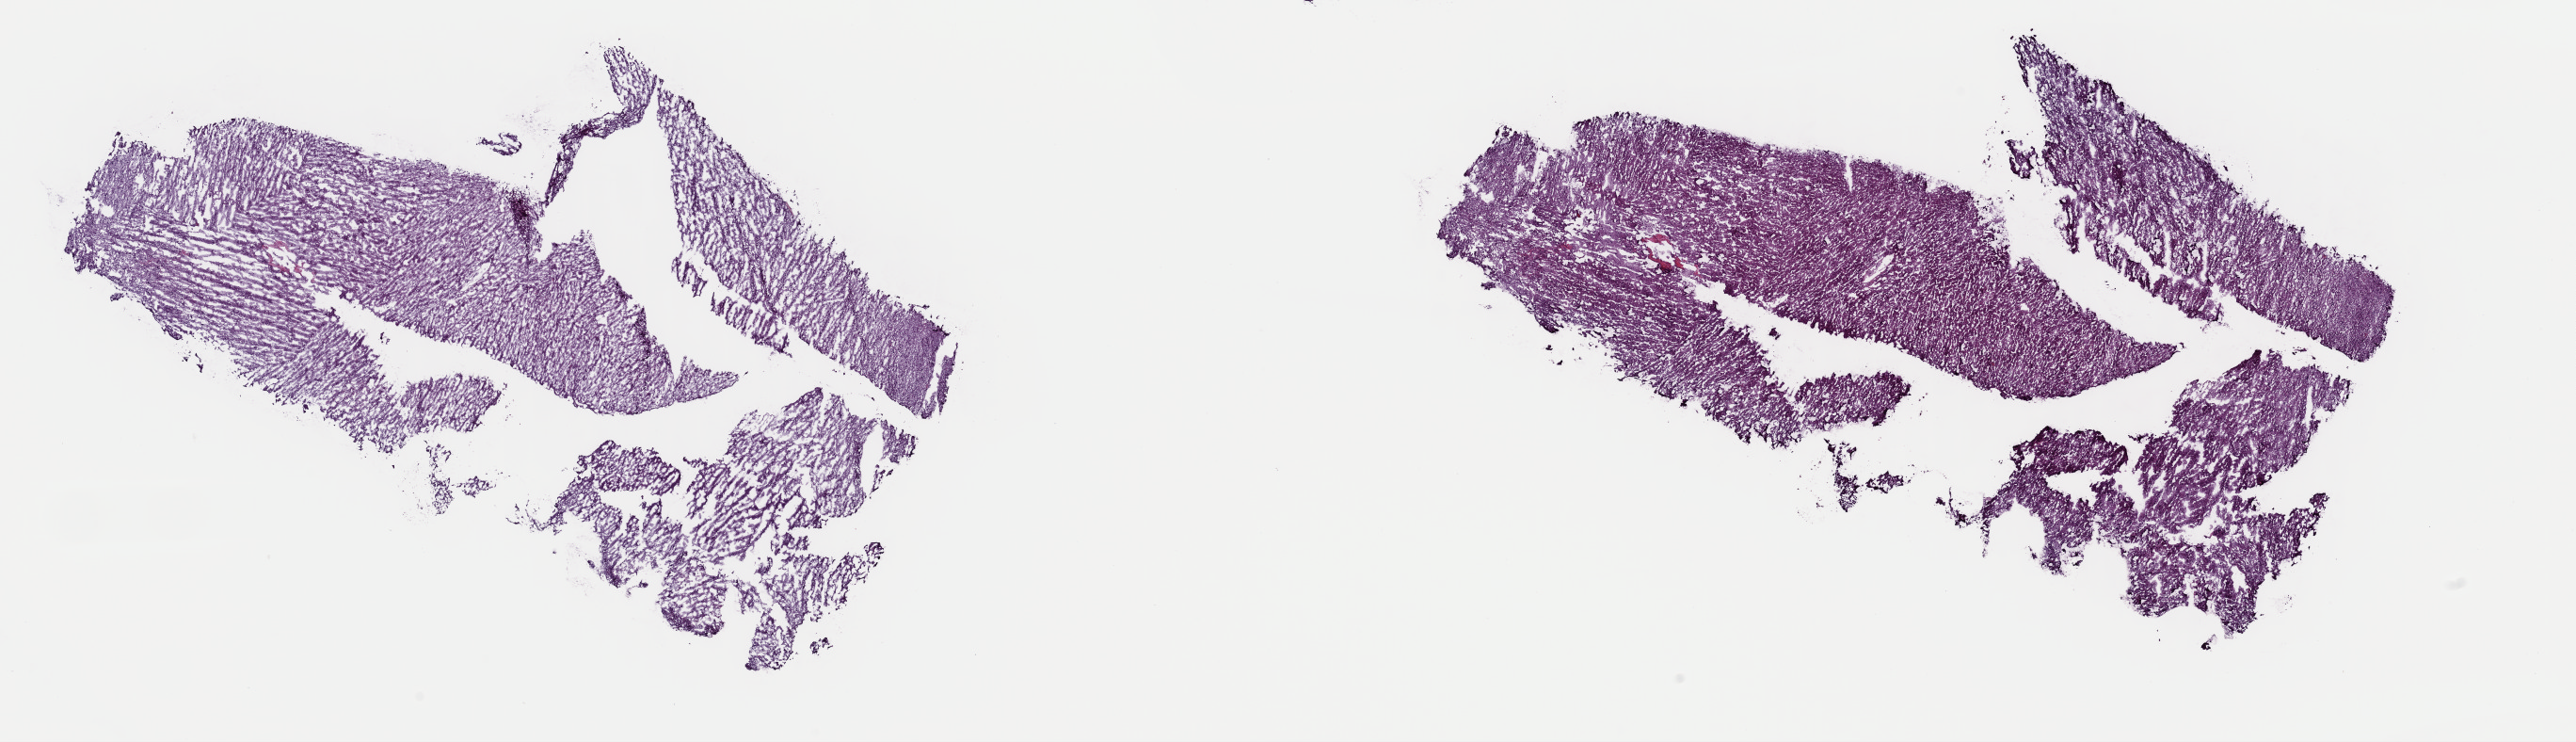
Digitized H&E tissue section (whole slide), a low-resolution overview of the entire scanned area, about 21.6 x 6.2 mm (from a 40x scan); frozen section from the top of the tissue portion; sample: primary tumour, adrenal cortex. Female patient; age at initial diagnosis 36 years. Pathologist review of this section (percent, as recorded): tumour cells 100%, tumour nuclei 97%, normal cells 0%, stromal cells 0%, necrosis 0%. Inflammatory infiltration, as recorded: lymphocyte infiltration 0%, monocyte infiltration 0%, neutrophil infiltration 0%.
Laterality: right. Diagnosis: Adrenal cortical carcinoma (cortex of adrenal gland).